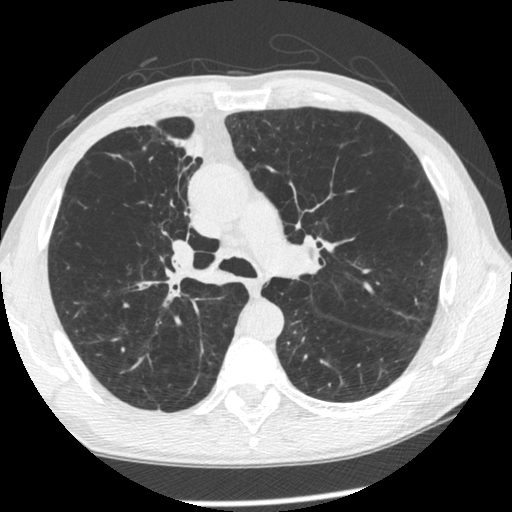
Low-dose screening chest CT, one axial slice; slice 152 of 261 in the series (ordered by position); reconstruction kernel STANDARD; 120 kVp; lung window (W 1500 / L -600 HU); 512 × 512 image matrix.
Structures marked on this image (manually delineated by an expert):
- lesion 1 (tumor, upper lobe of right lung): box from (x=173, y=134) to (x=203, y=159) px